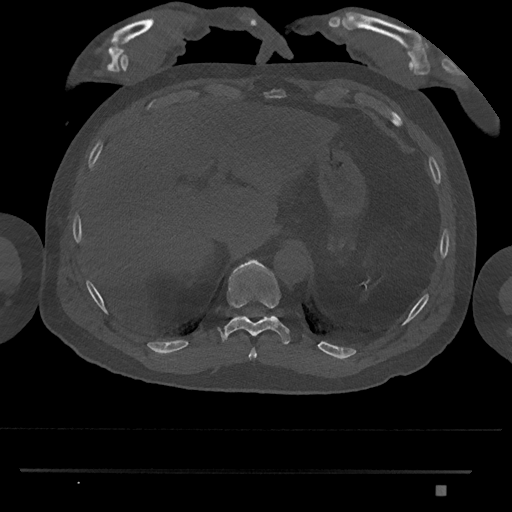
CT including the spine, one axial slice; position 998 of 1134 along the scan axis; reconstruction kernel Br40s/3; 120 kVp; bone window (W 1800 / L 400 HU); 0.5 mm slice thickness; 512 × 512 image matrix. Patient: male, 65 years. From the clinical record (not read from this slice): primary cancer: prostate.
Outlined on this slice (semi-automatic segmentation, software-assisted and operator-edited):
- T10 vertebra: box from (x=222, y=259) to (x=290, y=346) px
- T11 vertebra: (x=234, y=313)–(x=244, y=318)
- T9 vertebra: (x=248, y=348)–(x=257, y=360)